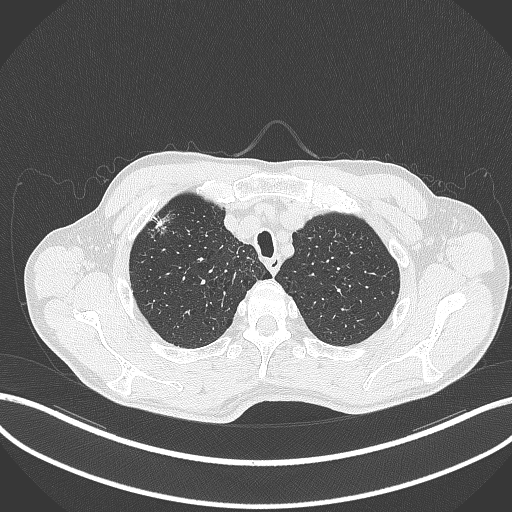
Chest CT, one axial slice. Slice 360 of 427 in the series (ordered by position). 120 kVp. Lung window (W 1500 / L -600 HU). 1 mm slice thickness. 512 × 512 image matrix. Patient: male, 69 years. From the clinical record (not read from this slice): clinical TNM (as recorded): T1b N1 M0.
Structures marked on this image (bounding box drawn by a radiologist):
- lung tumour (recorded histology: adenocarcinoma): box from (x=151, y=208) to (x=173, y=232) px